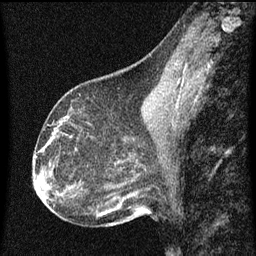
Breast MRI (dynamic contrast-enhanced), one sagittal slice. Slice 30 of 60 in the series (ordered by position). Dynamic contrast-enhanced series, image 2 of 3 at this slice position (ordered by acquisition). 1.5 T. TE 4.2 ms, TR 8 ms. 2 mm slice thickness. 256 × 256 image matrix, field of view 180 × 180 mm. Patient: female, 43 years.
Annotated regions visible in this slice (semi-automatic segmentation, software-assisted and operator-edited):
- analysis volume of interest (the breast-tissue region the enhancement analysis was run in; not a lesion): bounding box (x1, y1, x2, y2) in pixels: (53, 104, 101, 151)
- tumour enhancement mask (voxels above the 70 % enhancement threshold inside the analysis volume of interest): (59, 120, 72, 139)